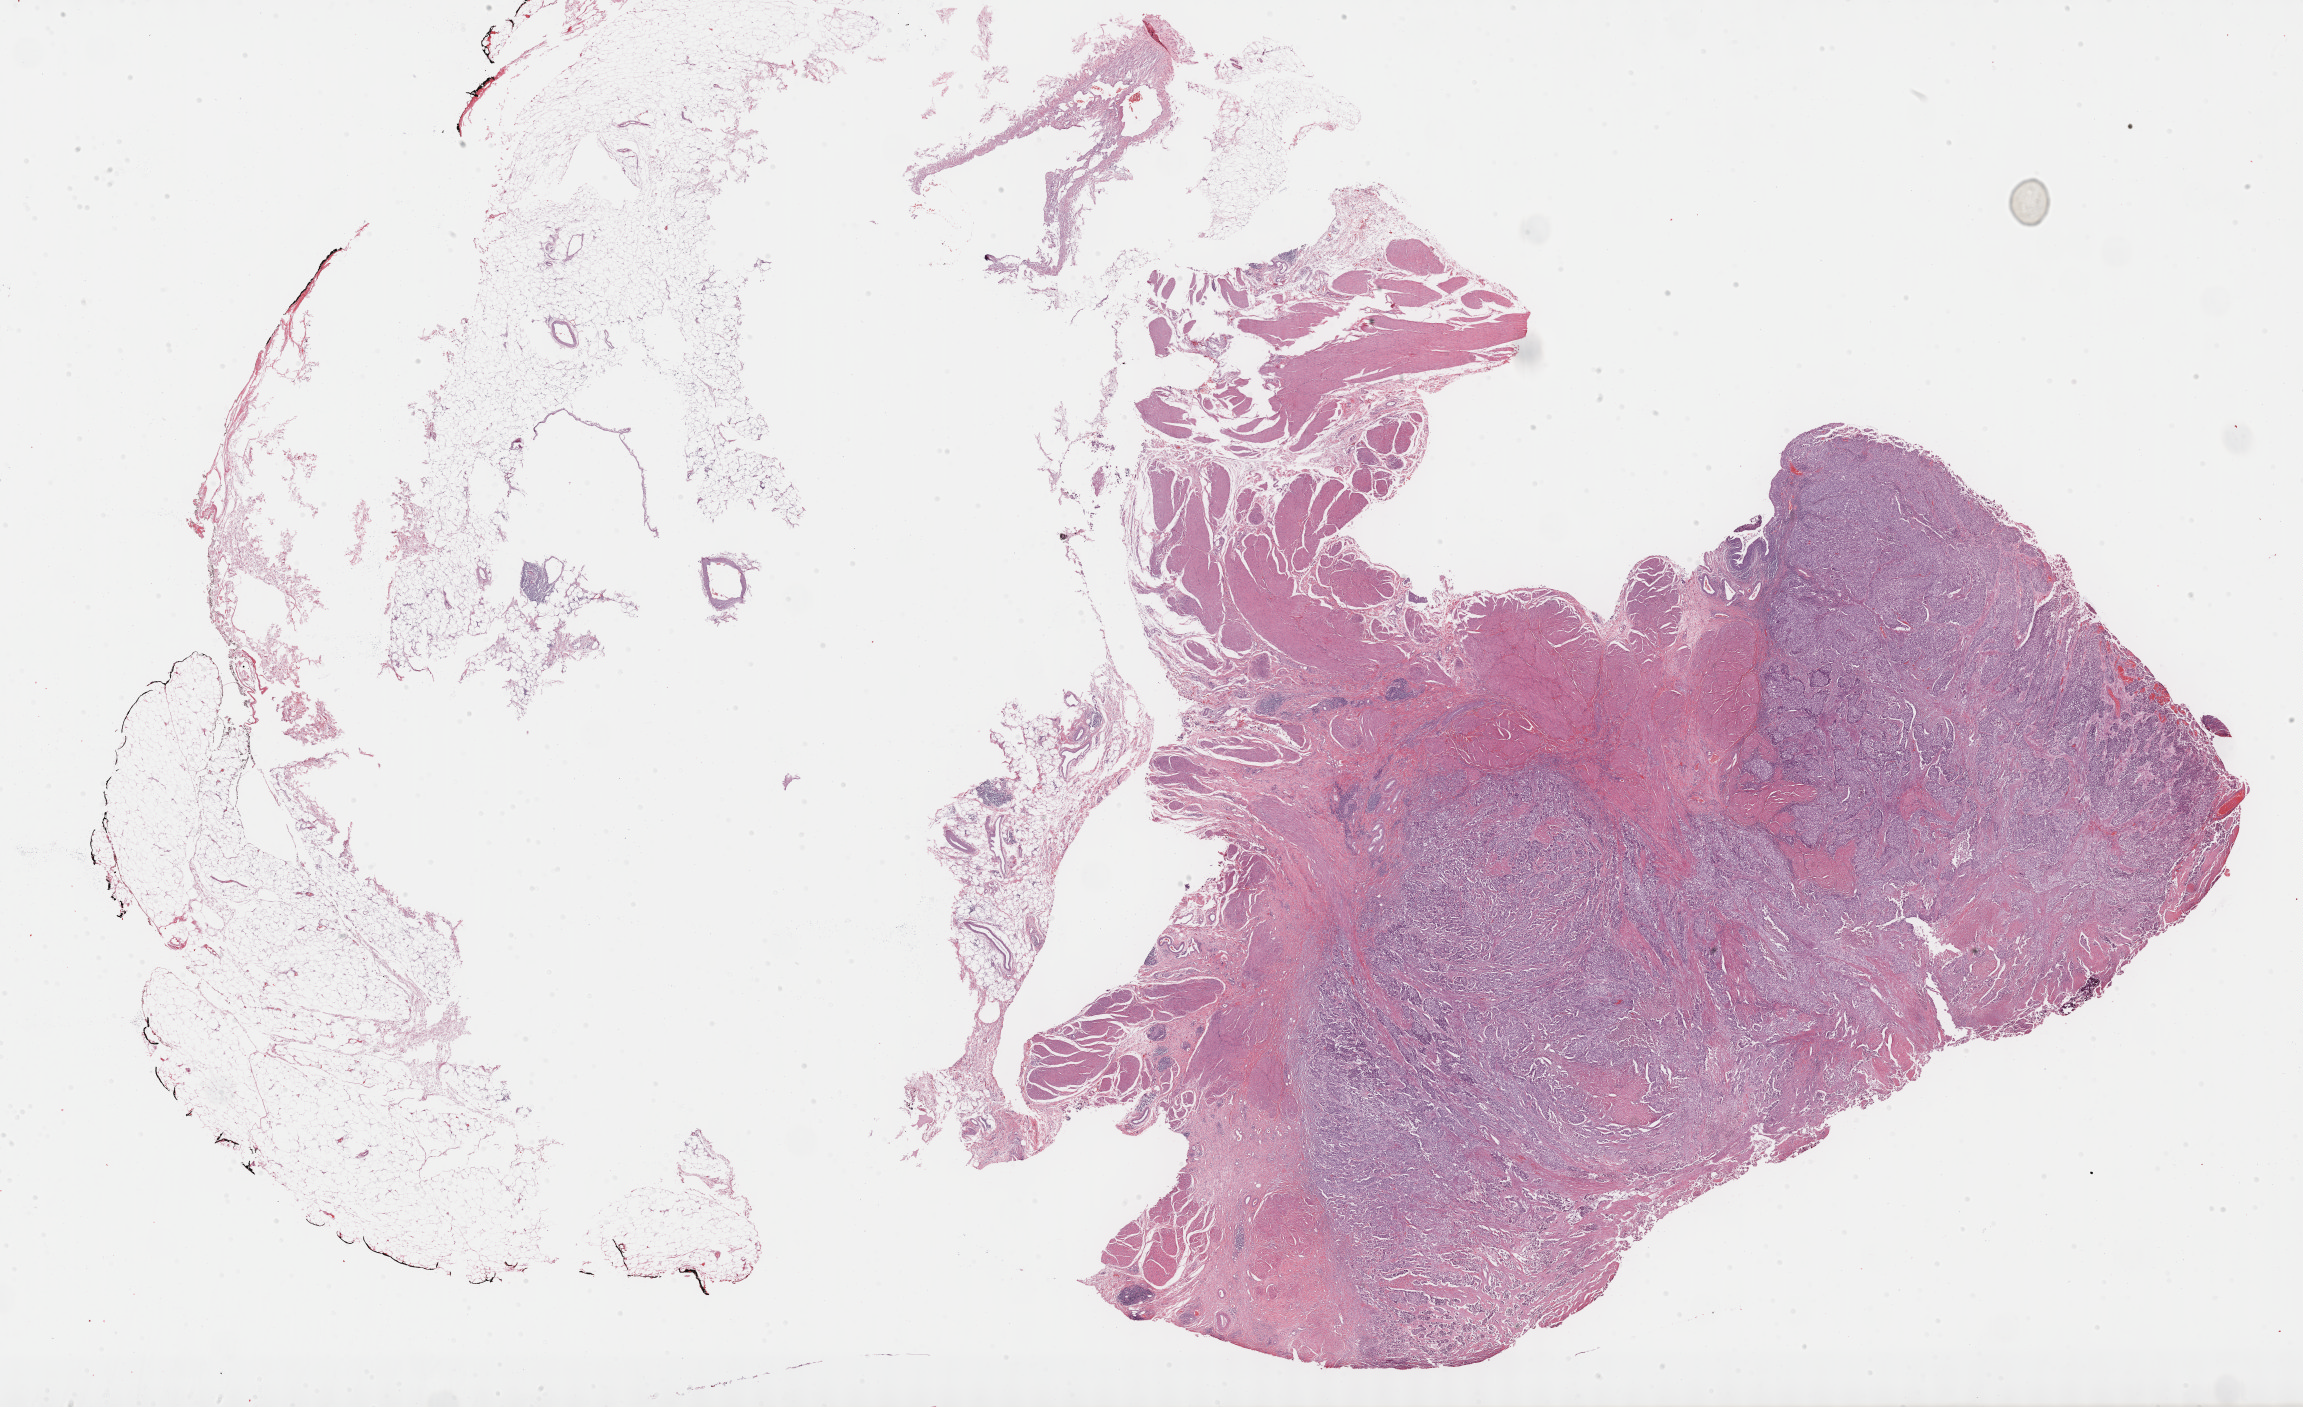
Hematoxylin and eosin (H&E) stained whole-slide image, shown as a low-resolution overview of the whole scanned area (about 37.2 x 22.8 mm, acquisition: 40x scan). FFPE section. Sample: primary tumour, bladder. Patient: male, age at initial diagnosis 68 years. Histologic grade: high grade.
* histologic diagnosis: Transitional cell carcinoma
* AJCC pathologic stage: III
* TNM: T3b N0 MX
* lymph nodes positive (case pathology): 0 of 79 examined